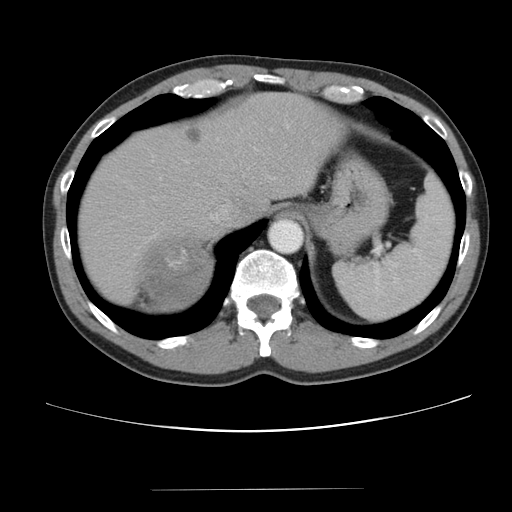
Contrast-enhanced abdominal CT, one axial slice. Slice 71 of 80 in the series (ordered by position). Reconstruction kernel STANDARD. 120 kVp. Soft-tissue window (W 400 / L 40 HU). 512 × 512 image matrix, field of view 360 × 360 mm. Male patient, age 61 years. From the clinical record (not read from this slice): diagnosis: adrenocortical carcinoma; tumour side: right adrenal.
Outlined on this slice (semi-automatic segmentation, software-assisted and operator-edited):
- mass: box from (x=141, y=234) to (x=210, y=307) px